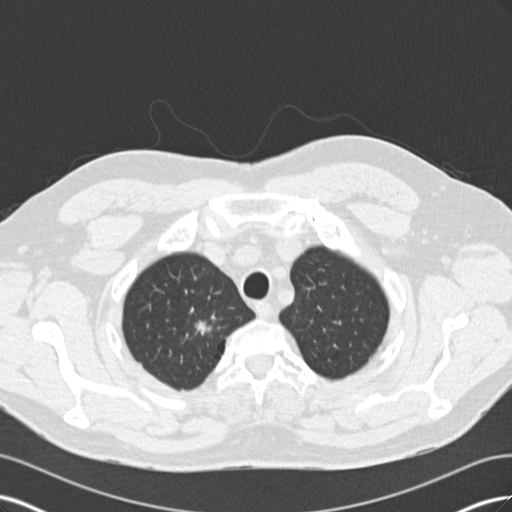
Axial slice from a low-dose chest CT screening exam, baseline screening round, lung window (W 1500 / L -600 HU), slice 22 of 171 in the series, 512 × 512 image matrix, field of view 360 × 360 mm. Male participant, aged 56 years at enrolment. Former smoker at enrolment.
Expert-annotated lung lesion, bounding box <175,309,225,353> (left, top, right, bottom; pixels). Screening reader's record for this exam (one nodule recorded; not confirmed to be the boxed lesion): non-calcified nodule or mass ≥4 mm, right upper lobe, 14 × 8 mm, spiculated (stellate) margins. Official screen result: positive, change unspecified: nodule(s) >= 4 mm or enlarging nodule(s), mass(es), or other non-specific abnormalities suspicious for lung cancer. Later outcome: lung cancer diagnosed 146 days after this screen — adenocarcinoma, NOS, right upper lobe, poorly differentiated (G3), stage IA (AJCC 6th edition), 12 mm at pathology.